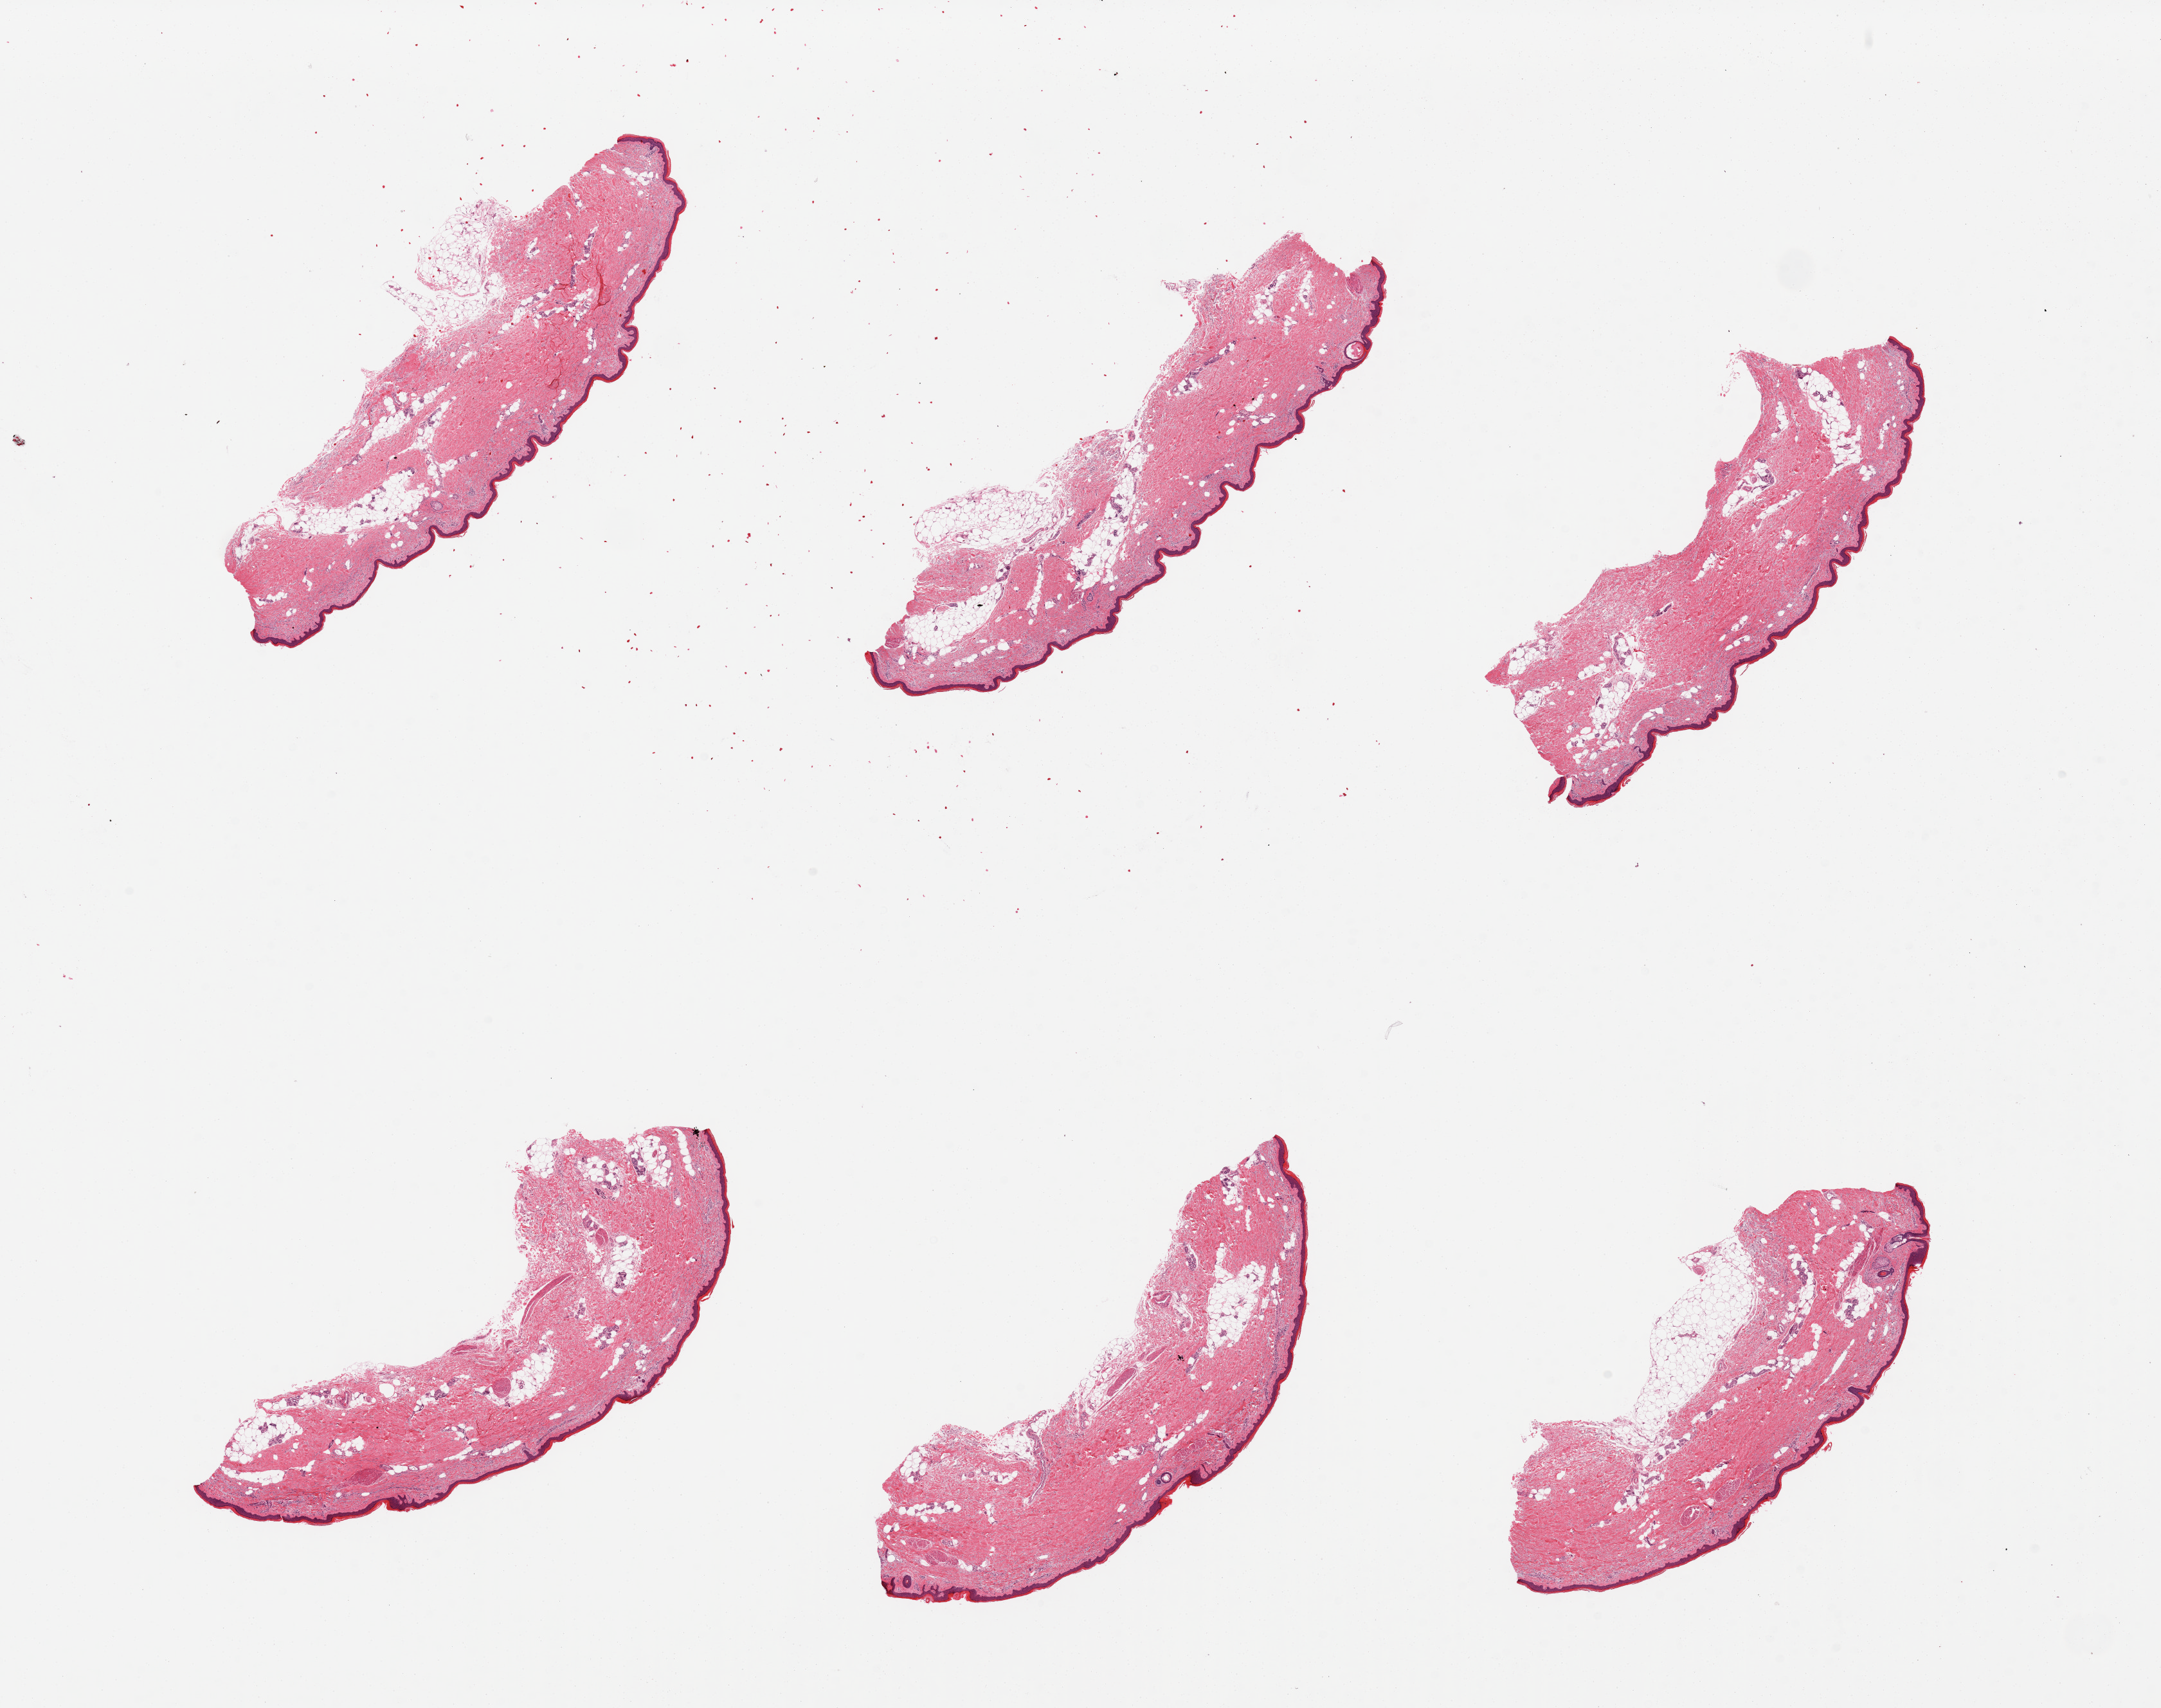
H&E whole-slide image — a low-resolution overview of the entire scanned area, about 26.6 x 21.0 mm (slide scanned at 20x). PAXgene-fixed paraffin-embedded (PFPE) section. Sampled site (target tissue): skin of lower leg. Tissue donor sample. Female donor.
Pathologist's review note for this sample: 6 pieces, minimal fat.